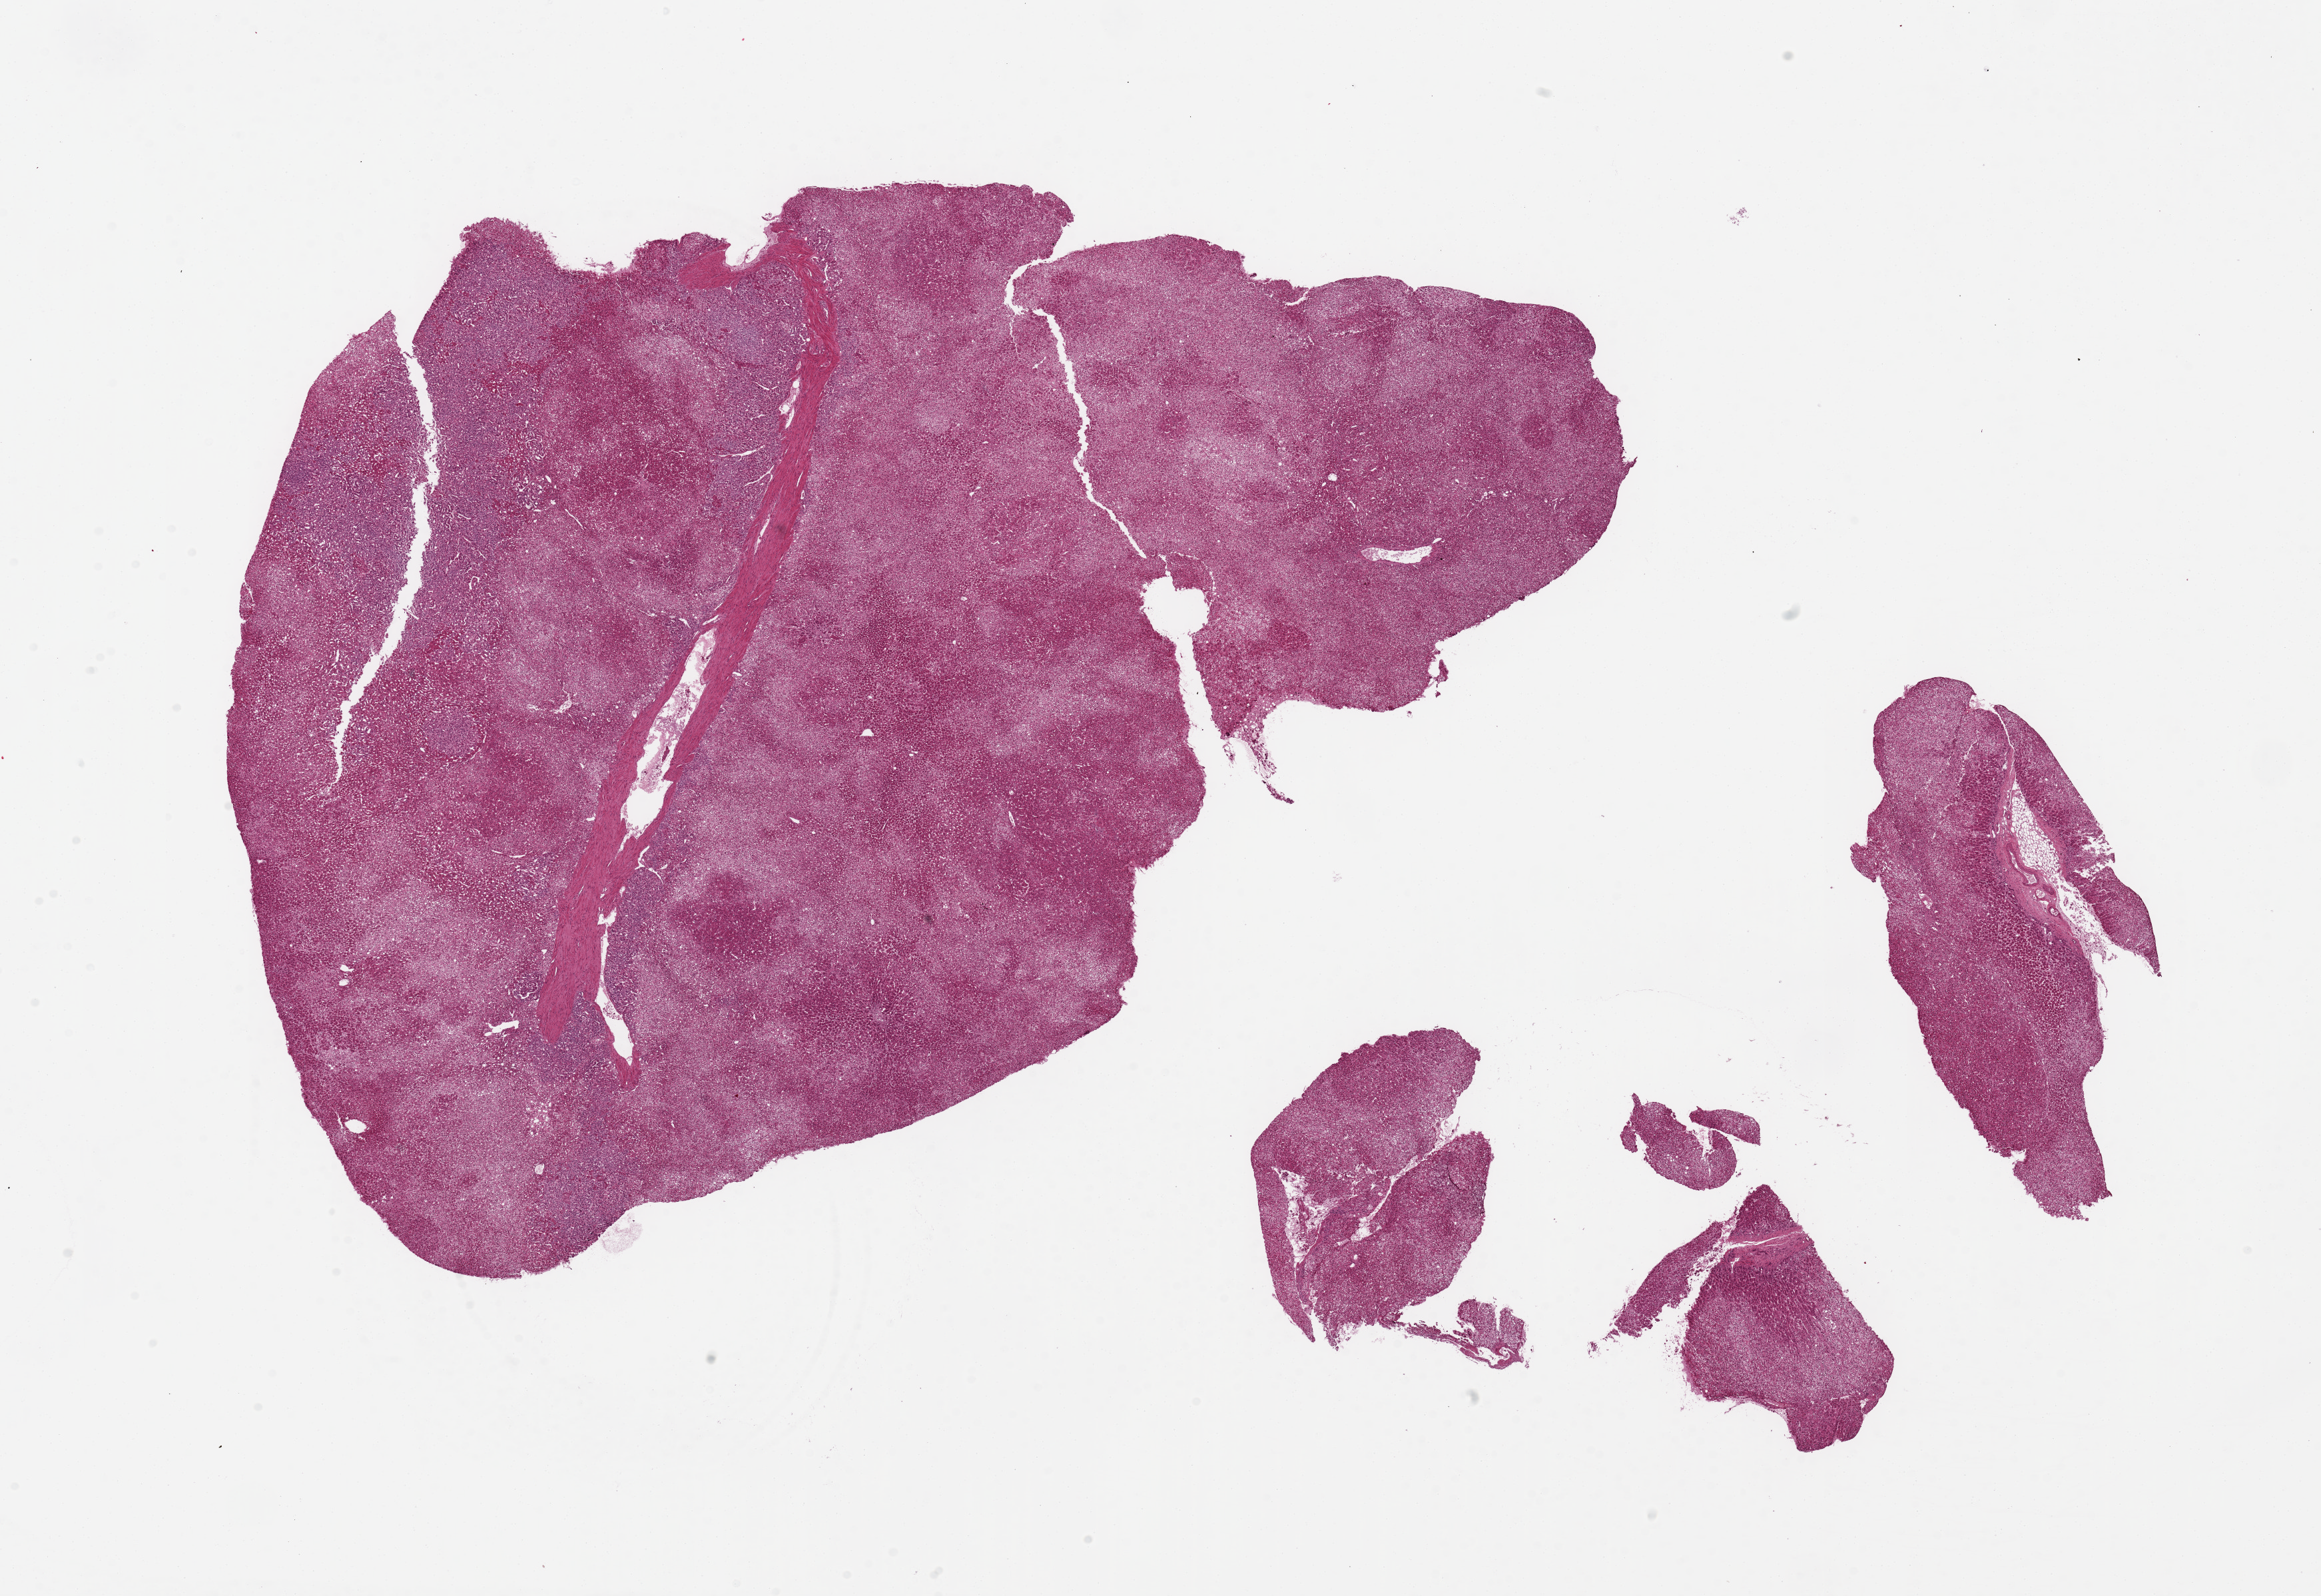
Digitized hematoxylin and eosin (H&E)-stained section — whole scanned area (about 27.6 x 19.0 mm, slide scanned at 20x) shown as a low-resolution overview, PAXgene-fixed paraffin-embedded (PFPE) section, sampled site (target tissue): adrenal gland, donor tissue sample. Donor: female.
• reviewer comment on this tissue sample: 2 pieces, 17x12.5 & 11x8mm; all cortex